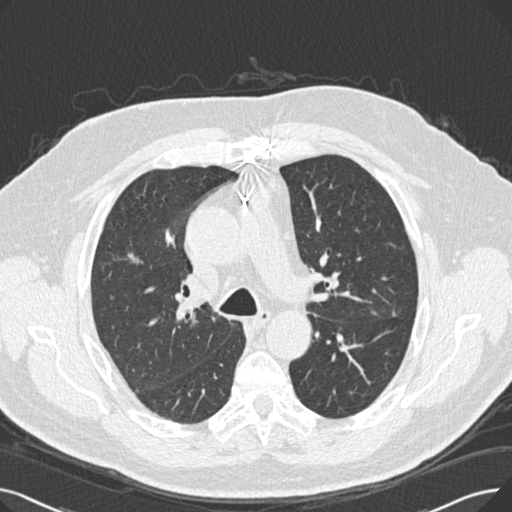
Low-dose screening chest CT, one axial slice; position 173 of 269 along the scan axis; reconstruction kernel B30f; 120 kVp; lung window (W 1500 / L -600 HU); 1 mm slice thickness; 512 × 512 image matrix, field of view 370 × 370 mm.
Annotated regions visible in this slice (manually delineated by an expert):
- lesion 1 (tumor, upper lobe of left lung): box from (x=392, y=311) to (x=396, y=316) px